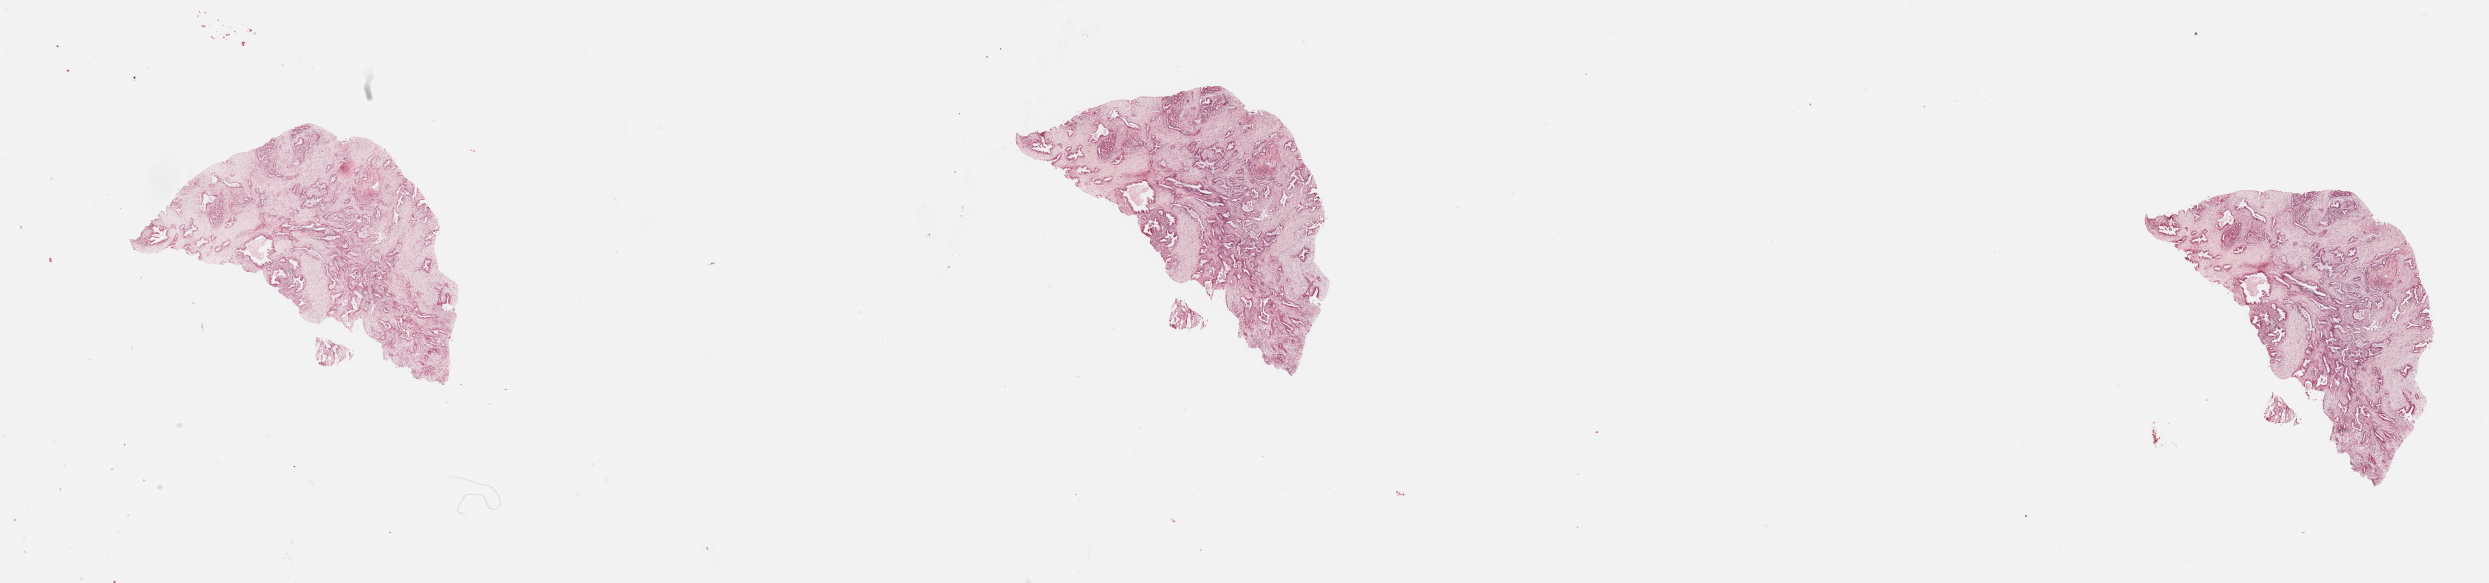
Whole-slide histology image, H&E, whole scanned area (about 39.4 x 9.2 mm) shown as a low-resolution overview, tumour tissue sample, sampled site: pancreas. 63-year-old male patient. Histologic grade: G2 (moderately differentiated). Composition of this section per pathologist review: tumour nuclei 20%, necrosis 0%.
Primary tumour site (as recorded): head. Diagnosis: Infiltrating duct carcinoma, NOS. AJCC pathologic stage: III.